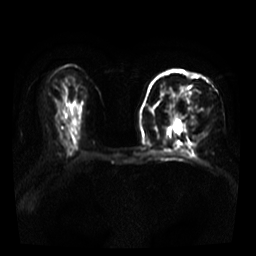
Breast MRI, one axial slice; slice 20 of 39 in the series (ordered by position); diffusion-weighted series; image 2 of 4 stored at this slice position (different b-values; order by instance number); 3 T; 5 mm slice thickness; 256 × 256 image matrix, field of view 320 × 320 mm. Female patient.
Annotated regions visible in this slice (manually delineated by an expert):
- tumour on diffusion-weighted imaging: bounding box (x1, y1, x2, y2) in pixels: (176, 86, 191, 119)